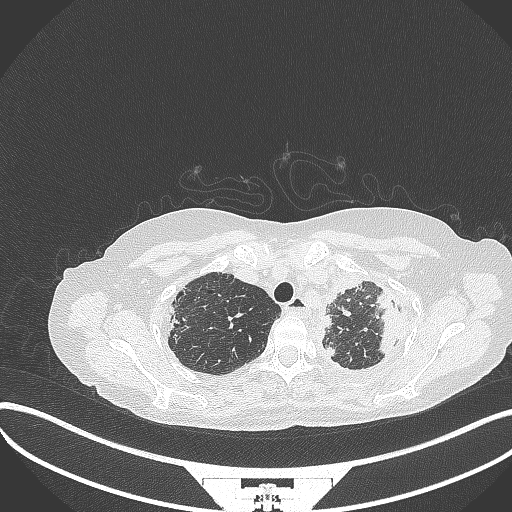
Chest CT, one axial slice; position 288 of 373 along the scan axis; 120 kVp; lung window (W 1500 / L -600 HU); 512 × 512 image matrix. Female patient, age 56 years. From the clinical record (not read from this slice): clinical TNM (as recorded): T1 N0 M0.
Annotated regions visible in this slice (rectangle marked by the reading radiologist):
- lung tumour (recorded histology: adenocarcinoma): bounding box (x1, y1, x2, y2) in pixels: (371, 290, 408, 364)